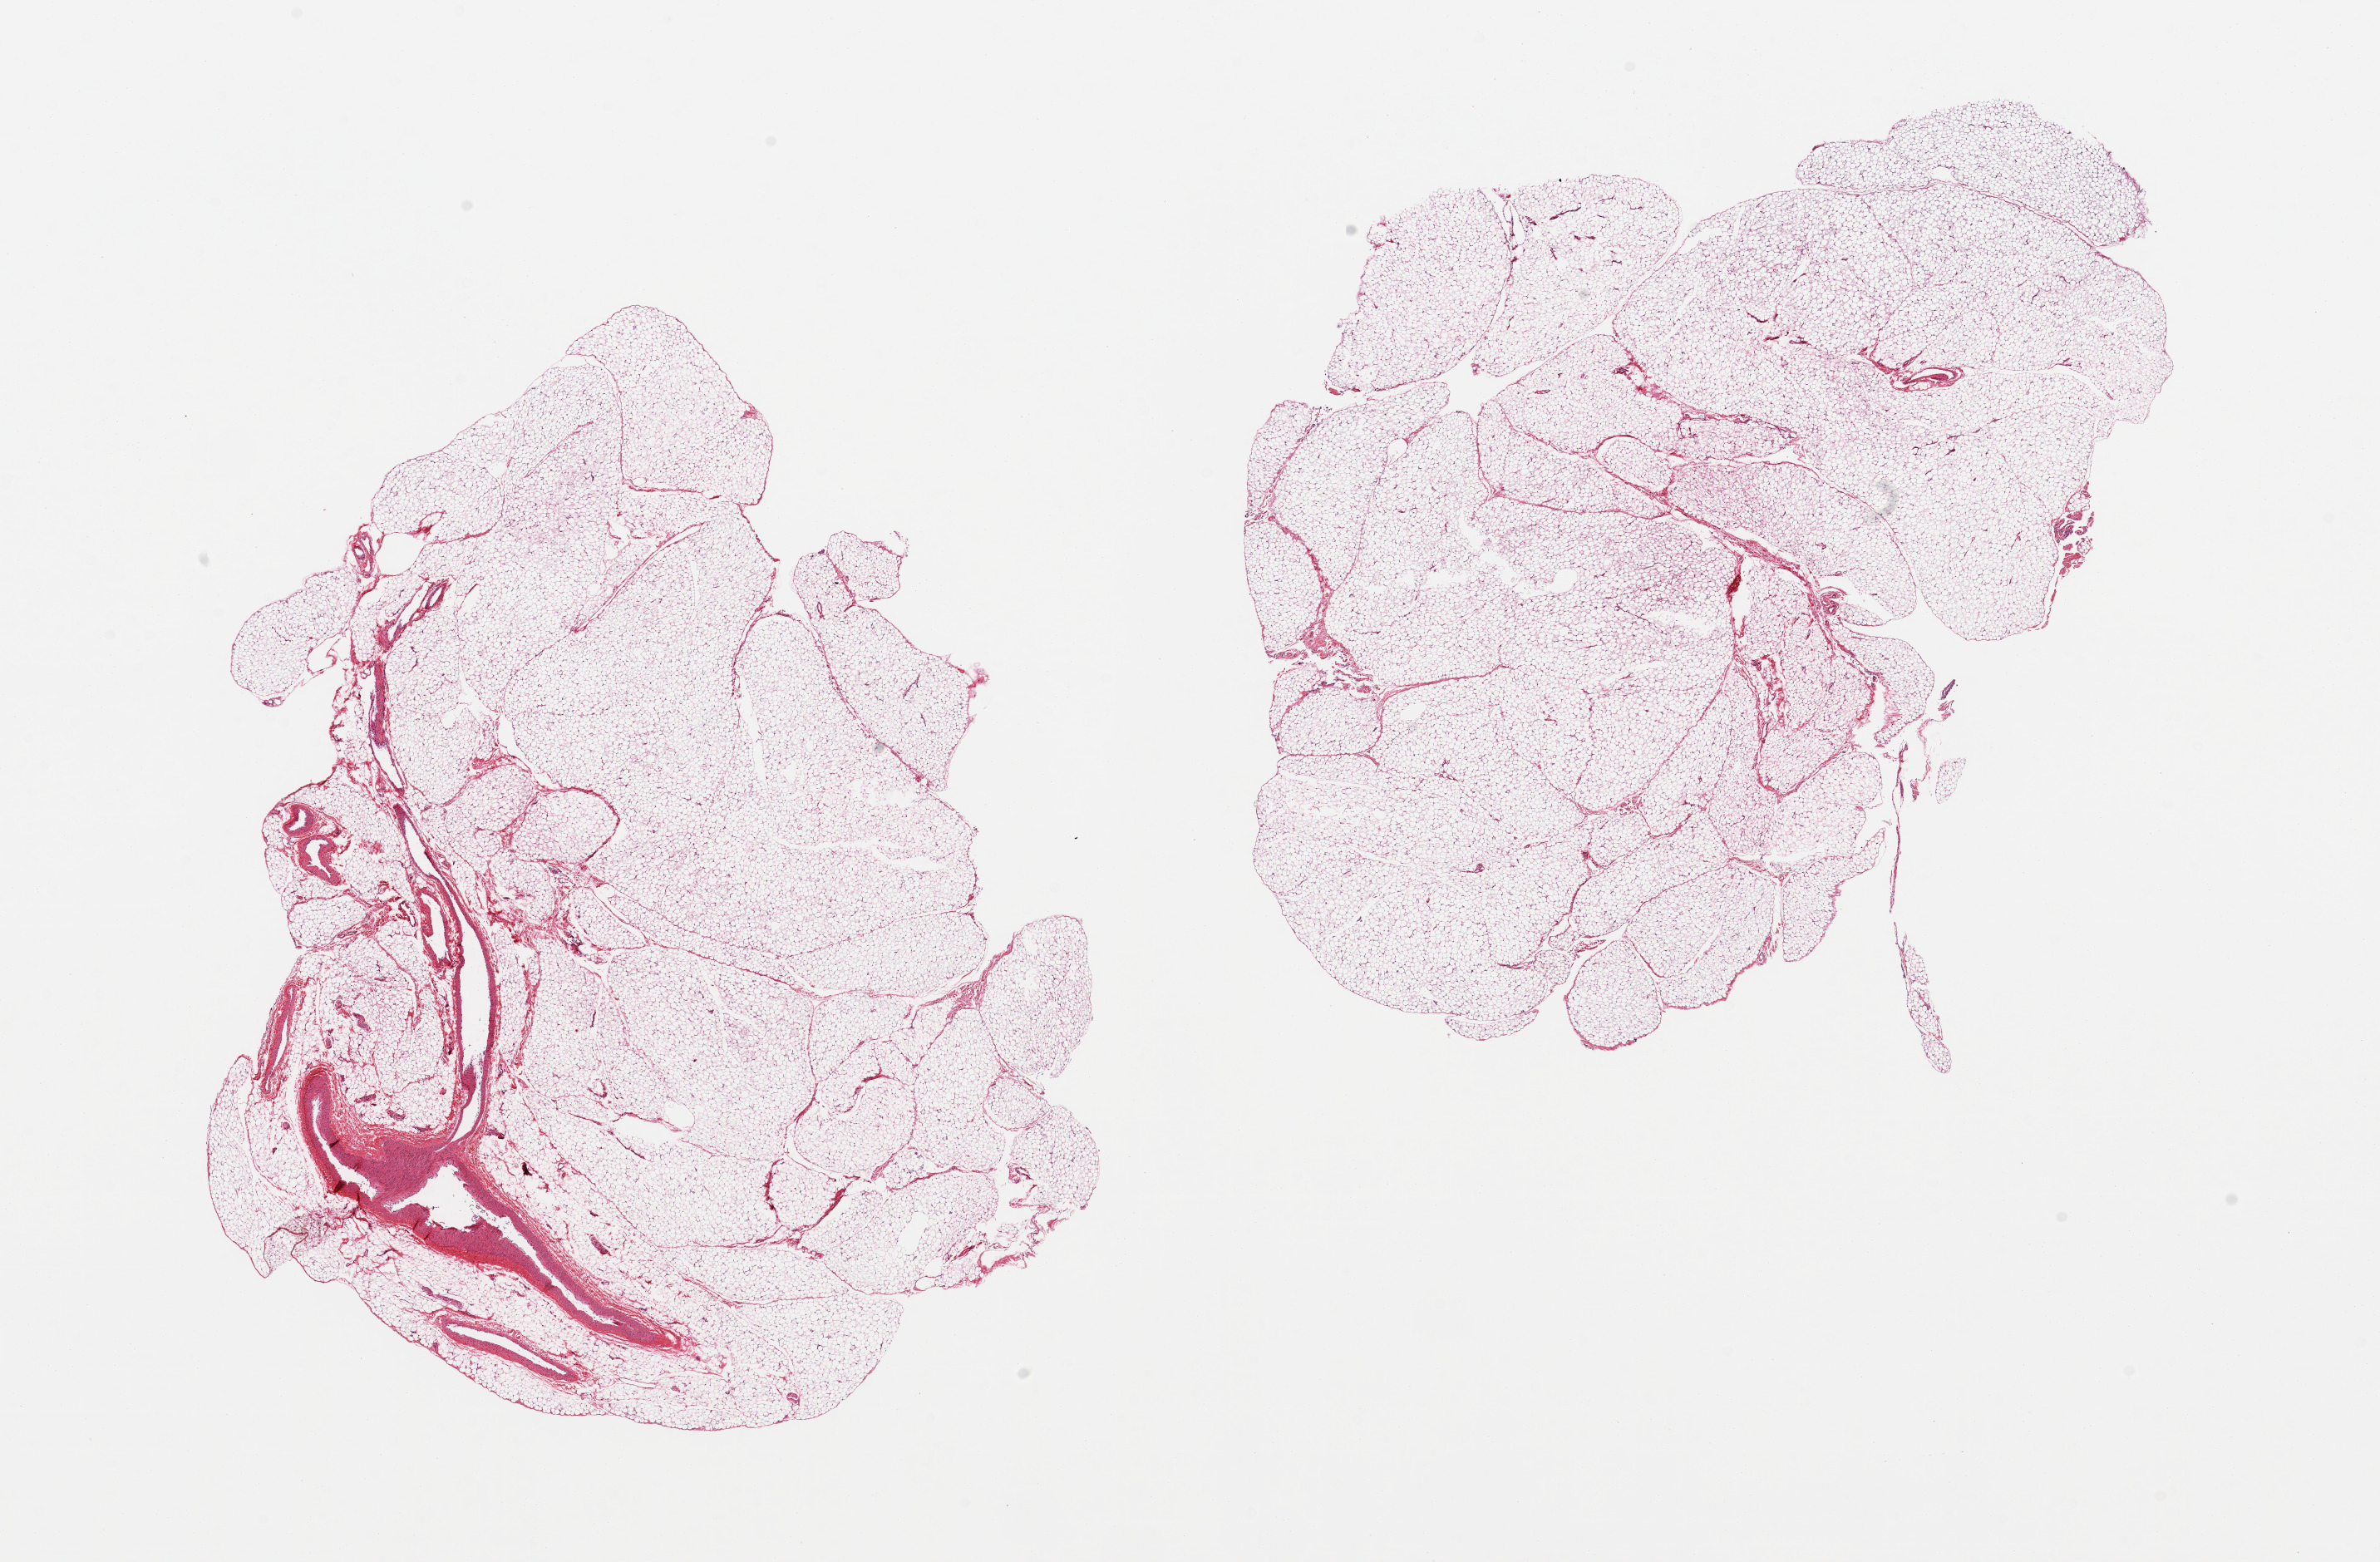
Digitized hematoxylin and eosin (H&E)-stained section, shown as a low-resolution overview of the whole scanned area (about 22.6 x 14.9 mm, slide scanned at 20x); PAXgene-fixed paraffin-embedded (PFPE) section; target tissue: omentum; donor tissue sample. Donor: male.
Reviewer comment on this tissue sample: 2 pieces, vascular elements are ~5-10% of tissue.